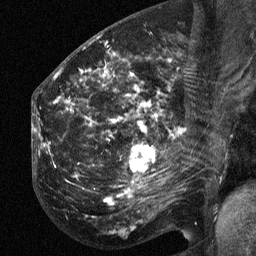
Breast MRI (dynamic contrast-enhanced), one sagittal slice; position 30 of 64 along the scan axis; dynamic contrast-enhanced study with each time point stored as its own series, time point 2 of 3 at this slice position (early post-contrast, ordered by acquisition time); 1.5 T; TE 4.8 ms, TR 27 ms; 256 × 256 image matrix, field of view 200 × 200 mm. Patient: female, 50 years. From the clinical record (not read from this slice): setting: breast cancer imaged before/during neoadjuvant chemotherapy; receptor status: HER2-positive.
Annotated regions visible in this slice (semi-automatically segmented with operator editing):
- analysis volume of interest (the breast-tissue region the enhancement analysis was run in; not a lesion): bounding box [x1, y1, x2, y2] px = [53, 64, 201, 213]
- tumour enhancement mask (voxels above the 90 % enhancement threshold inside the analysis volume of interest): [125, 145, 151, 192]